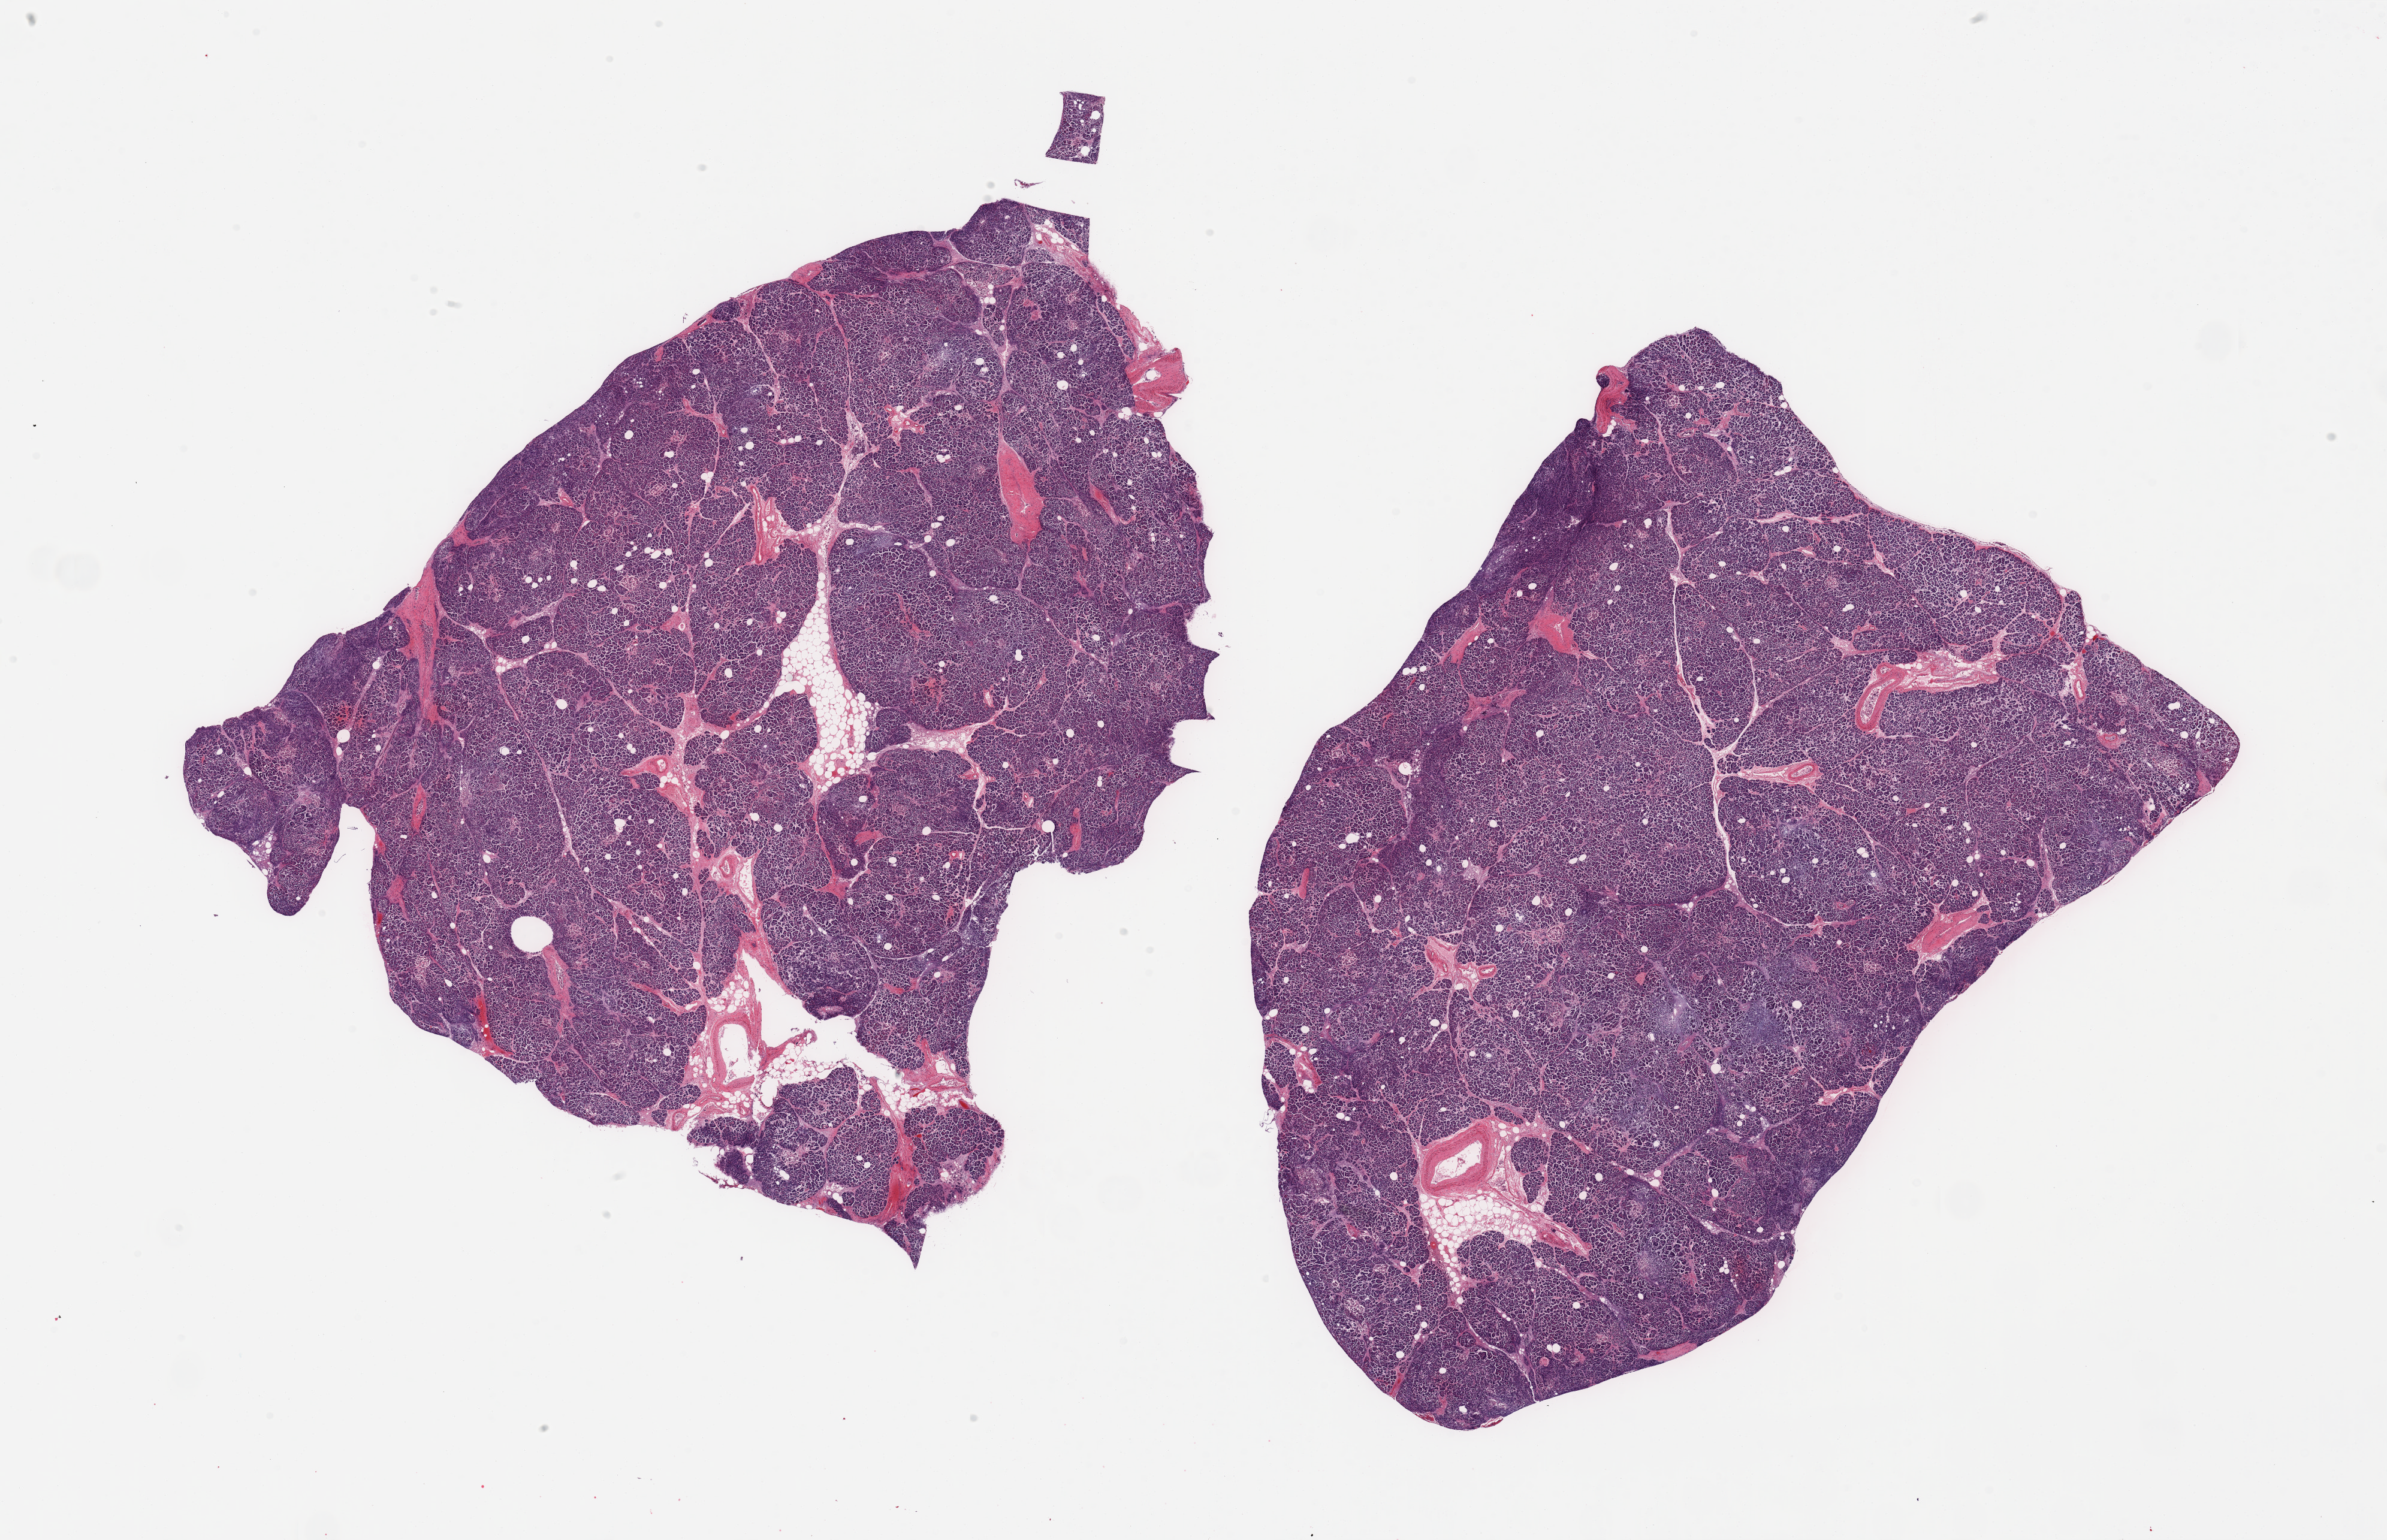
Digitized hematoxylin and eosin (H&E)-stained section, brightfield — a low-resolution overview of the entire scanned area, about 31.5 x 20.3 mm; PAXgene-fixed, paraffin-embedded tissue; sampled site (target tissue): pancreas; tissue donor sample. Donor sex: male.
Pathologist's review note for this sample: 2 pieces; moderate to severe autolysis, minimal internal fat.